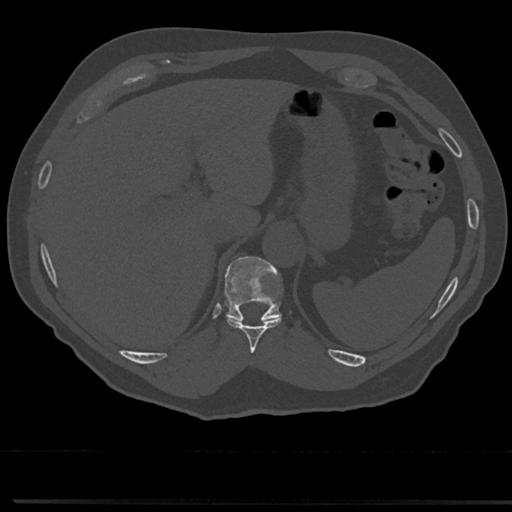
CT including the spine, one axial slice; slice 233 of 817 in the series (ordered by position); reconstruction kernel Br40s/3; 120 kVp; bone window (W 1800 / L 400 HU); 0.5 mm slice thickness; 512 × 512 image matrix, field of view 355 × 355 mm. Male patient, age 61 years. Case-level facts recorded for this patient, not image findings: primary cancer: prostate.
Outlined on this slice (semi-automatic segmentation, software-assisted and operator-edited):
- T10 vertebra: bounding box (x1, y1, x2, y2) in pixels: (226, 317, 283, 352)
- T11 vertebra: (226, 257, 281, 322)